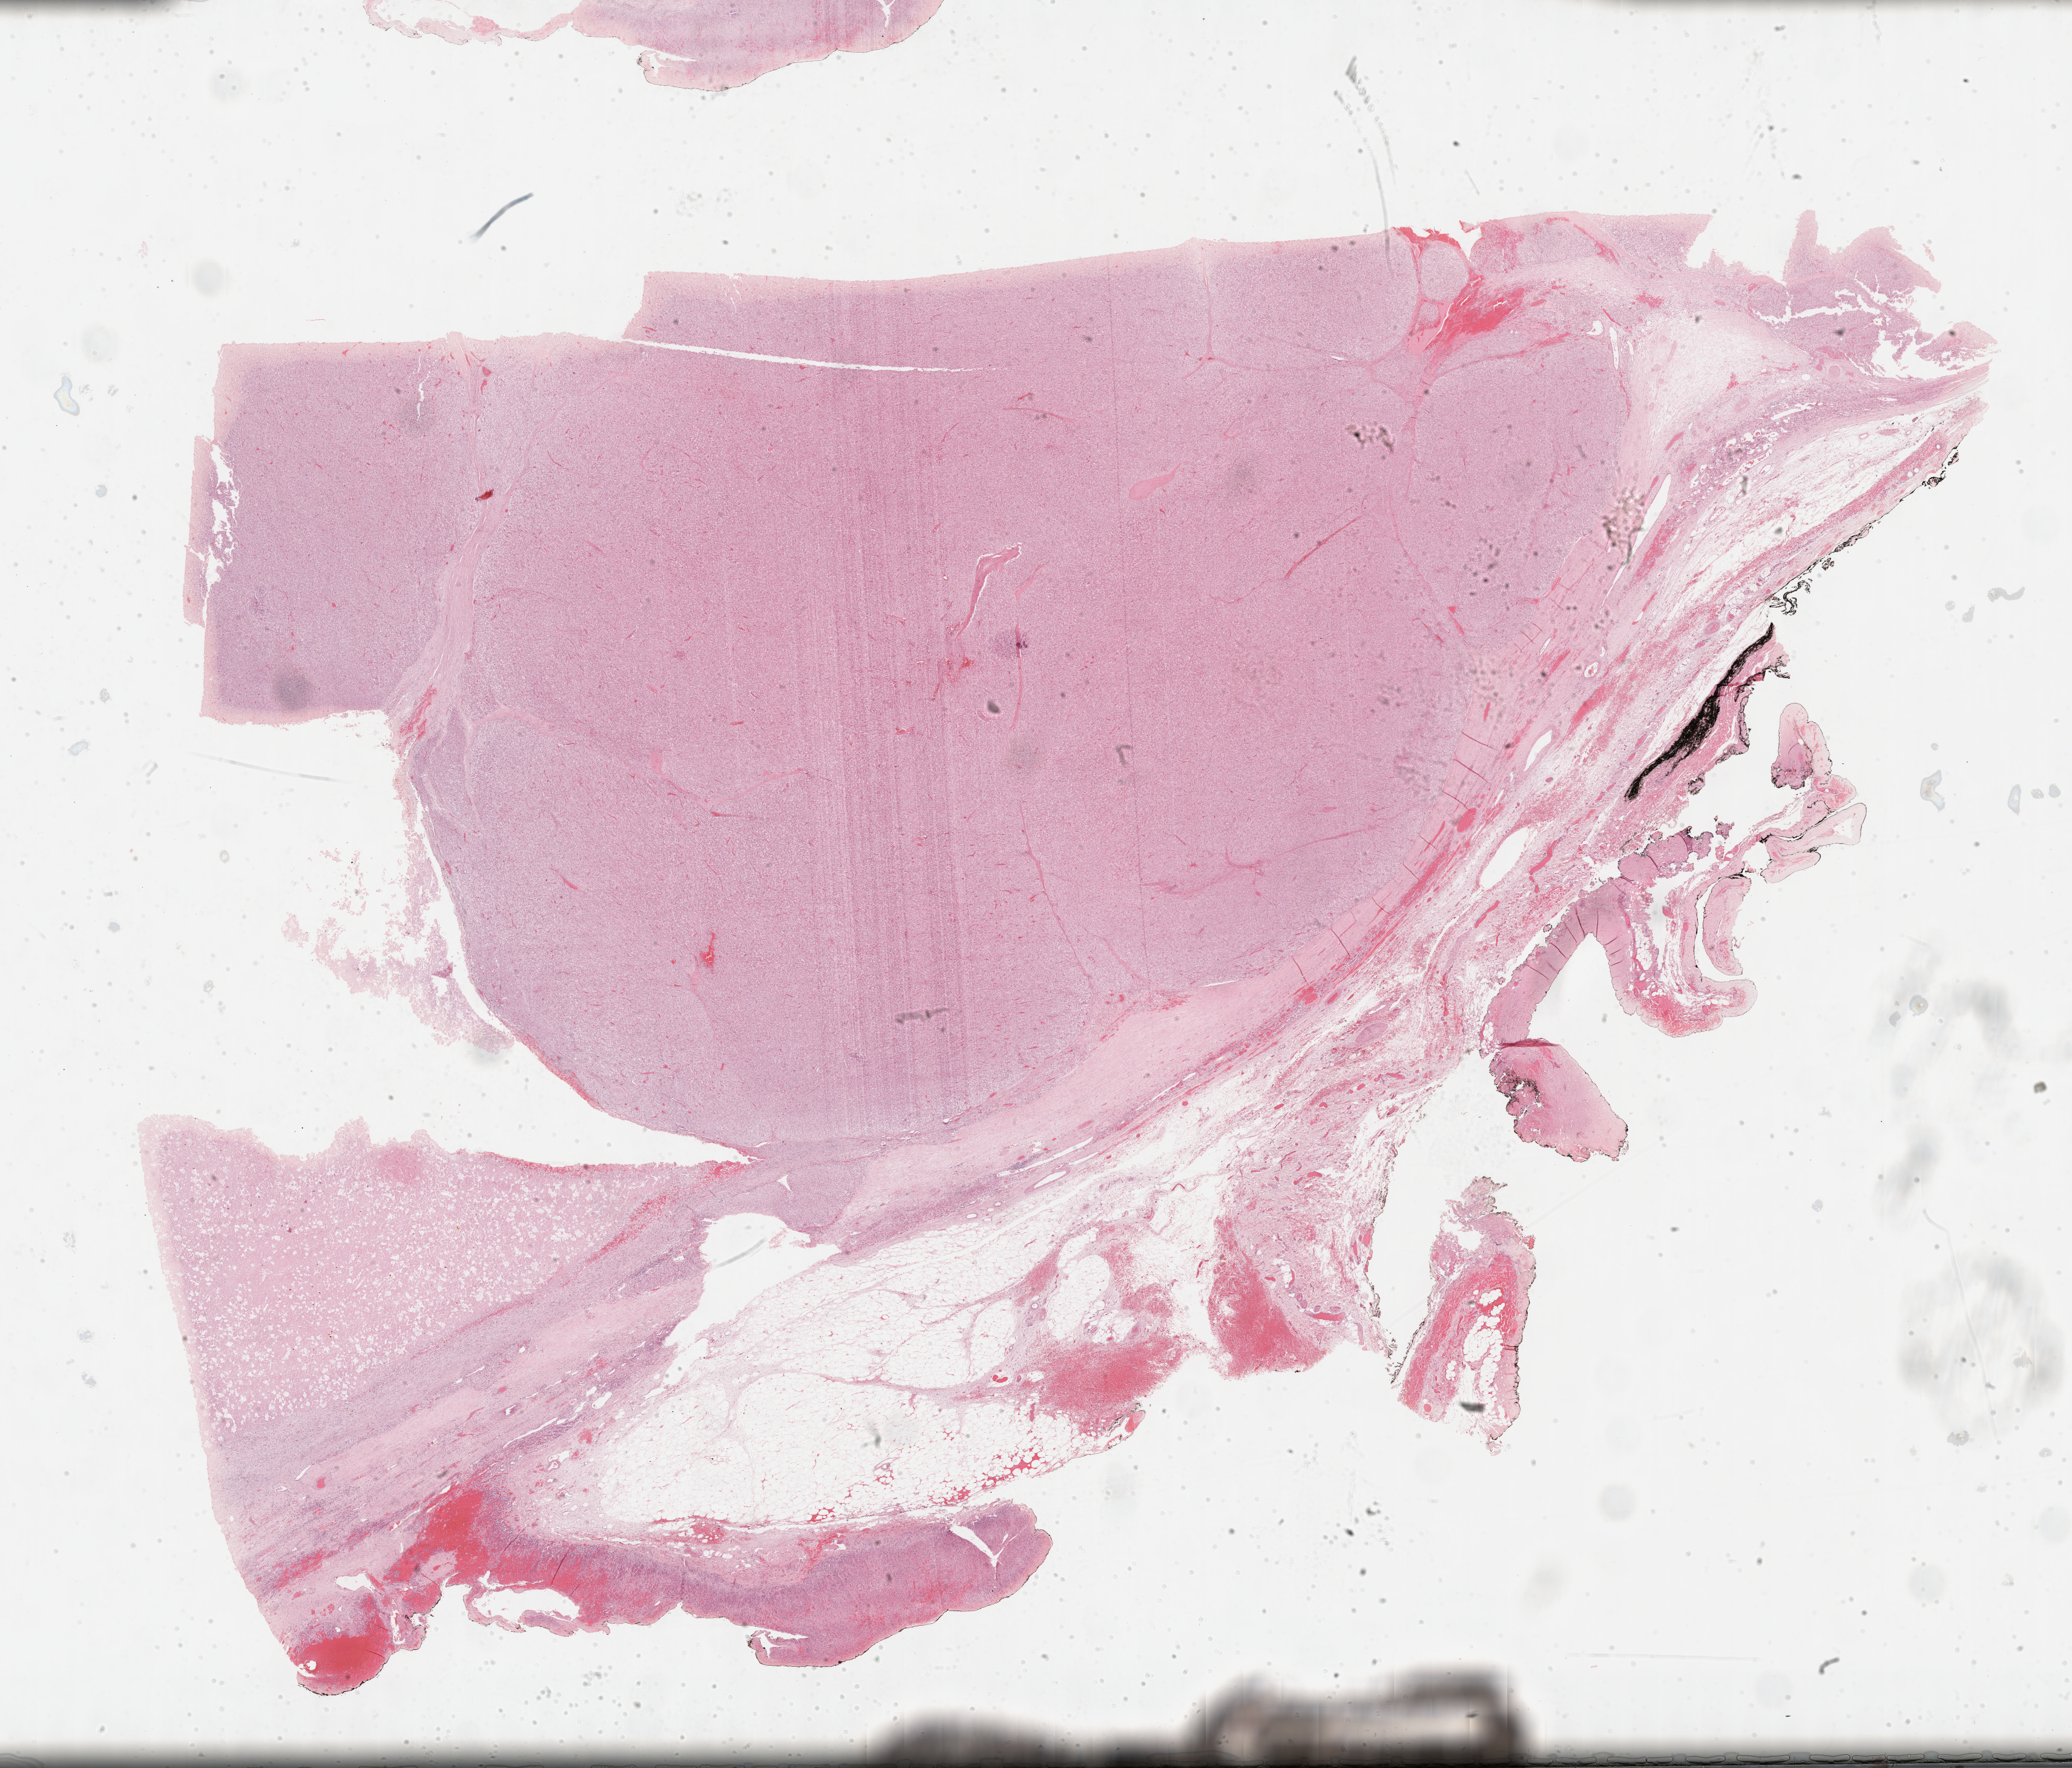
Digitized Hematoxylin and eosin (H&E) stained tissue section (whole slide), whole scanned area (about 27.7 x 23.6 mm, from a 40x scan) shown as a low-resolution overview. FFPE section. Adrenal cortex, primary tumour sample. Male patient; age at initial diagnosis 48 years.
Laterality: left. Diagnosis: Adrenal cortical carcinoma (cortex of adrenal gland).